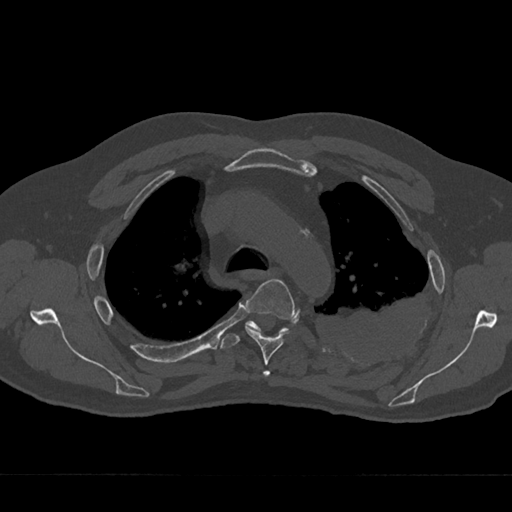
CT including the spine, one axial slice; position 509 of 797 along the scan axis; 120 kVp; bone window (W 1800 / L 400 HU); 512 × 512 image matrix, field of view 377 × 377 mm. Patient: male, 75 years. From the clinical record (not read from this slice): primary cancer: renal.
Structures marked on this image (semi-automatically segmented with operator editing):
- T3 vertebra: box from (x=263, y=371) to (x=270, y=376) px
- T4 vertebra: (x=245, y=279)–(x=295, y=377)
- T5 vertebra: (x=220, y=320)–(x=288, y=349)